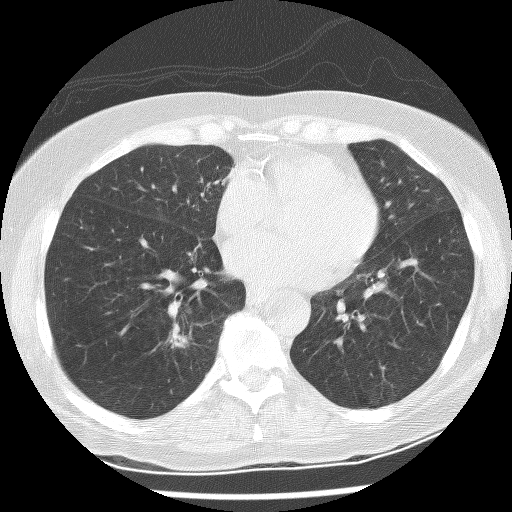
Low-dose screening chest CT, one axial slice. Slice 102 of 247 in the series (ordered by position). Lung window (W 1500 / L -600 HU). 2.5 mm slice thickness. 512 × 512 image matrix, field of view 300 × 300 mm.
Structures marked on this image (outlined manually by an expert reader):
- lesion 1 (tumor, lower lobe of right lung): box from (x=169, y=322) to (x=190, y=348) px